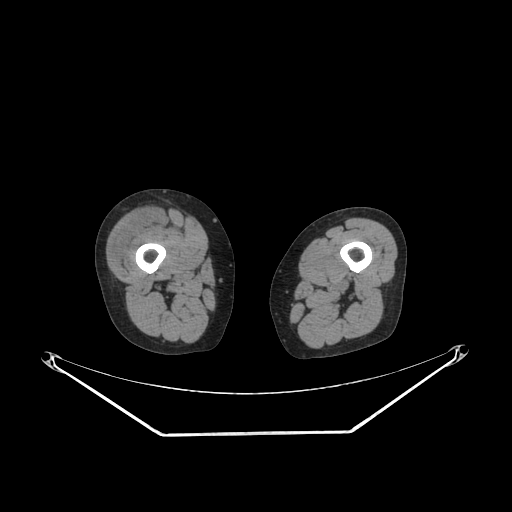
CT of an extremity soft-tissue mass (from a PET/CT study), one axial slice. Position 214 of 311 along the scan axis. 140 kVp. Soft-tissue window (W 400 / L 40 HU). 3.75 mm slice thickness. 512 × 512 image matrix, field of view 500 × 500 mm. Female patient. Case-level facts recorded for this patient, not image findings: histological type: pleiomorphic undifferentiated sarcoma; grade: high; site of the primary tumour: right quadricep.
Outlined on this slice (expert contour drawn on MRI and transferred to this co-registered scan by the dataset authors):
- tumour plus oedema (research contour): bounding box (x1, y1, x2, y2) in pixels: (110, 210, 161, 261)